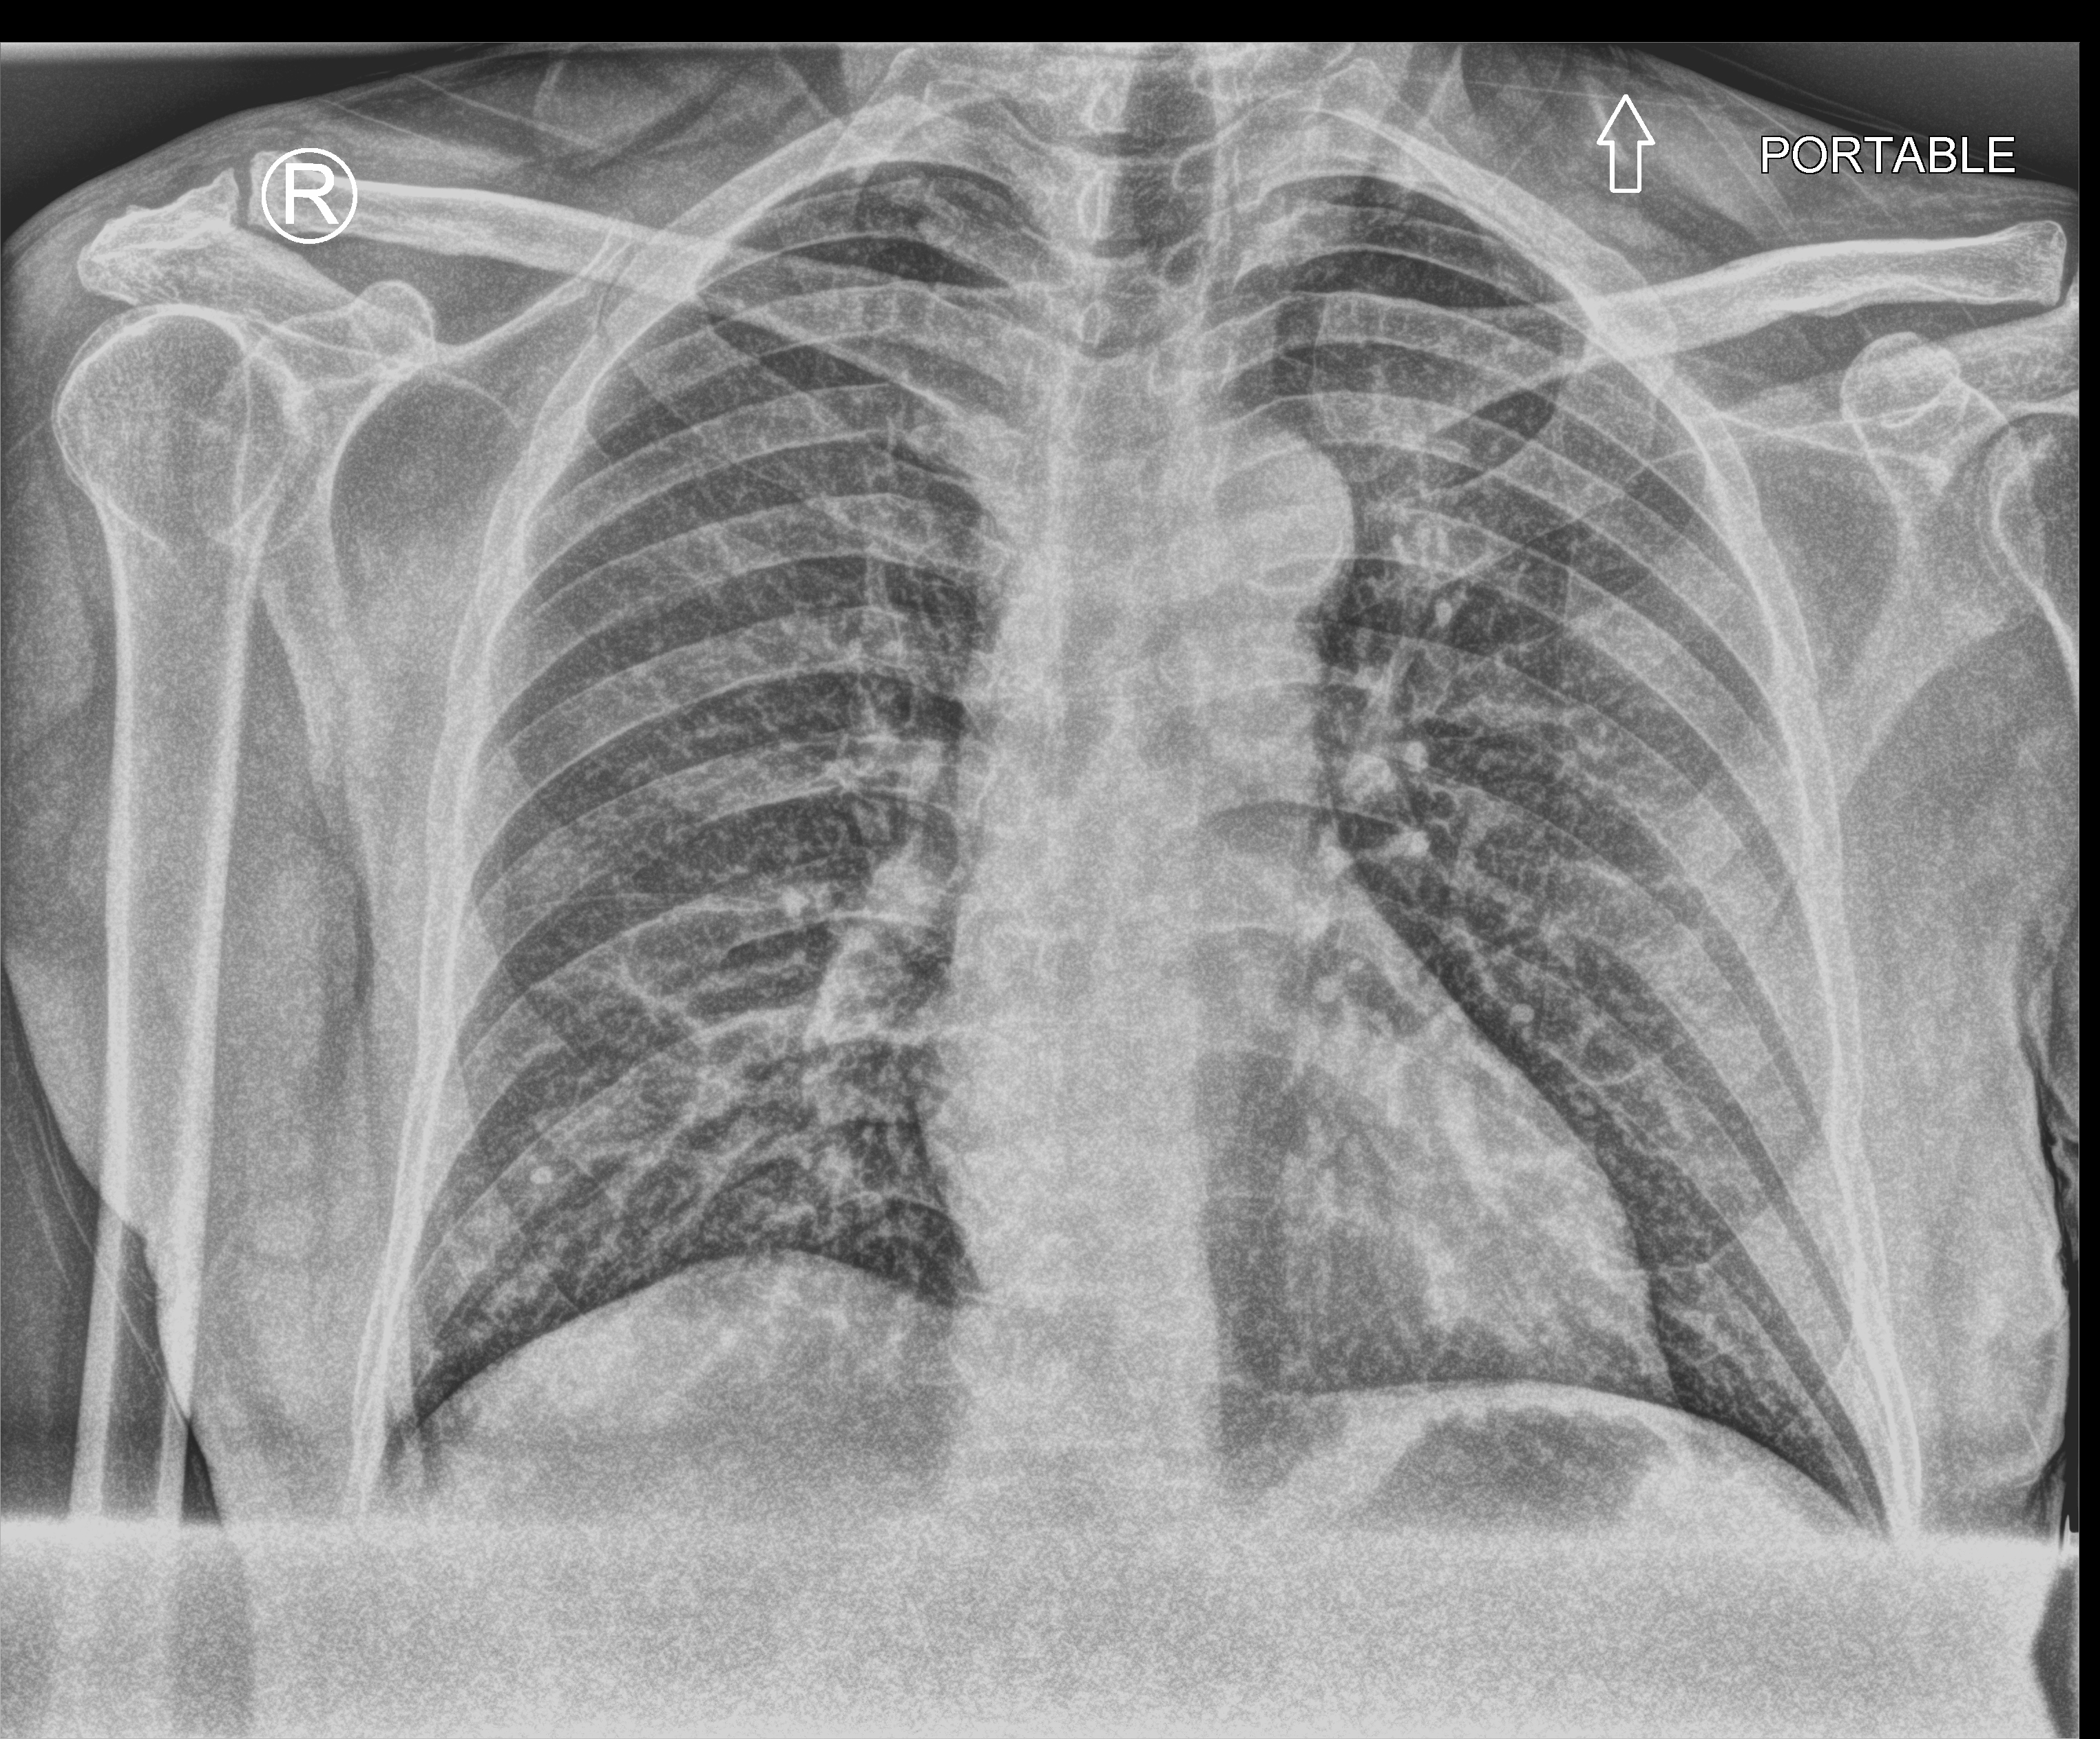
Chest X-ray (portable); anteroposterior (AP) projection. Patient hospitalised with COVID-19; male, aged 60–74 years.
From the hospital-stay record, not from the radiograph (when in the stay this image was taken is not recorded):
- smoking status (admission record): former